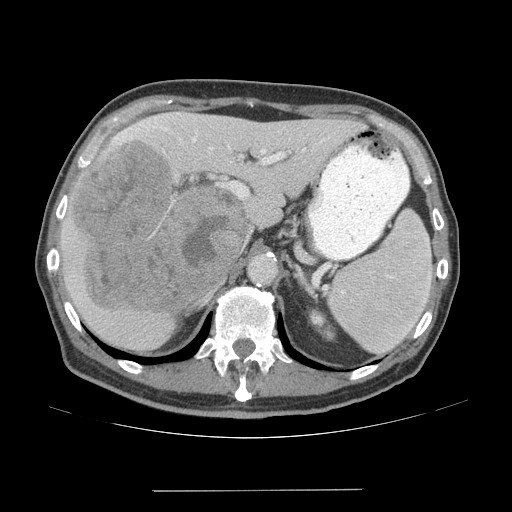
Contrast-enhanced abdominal CT (liver protocol), one axial slice; reconstruction kernel STANDARD; 140 kVp; soft-tissue window (W 400 / L 40 HU); 2.5 mm slice thickness; 512 × 512 image matrix. Case-level facts recorded for this patient, not image findings: diagnosis: hepatocellular carcinoma (patient treated with transarterial chemoembolisation; whether this scan precedes or follows treatment is not stated here); TNM stage (as recorded): Stage-IVA; Child-Pugh class: A; tumour nodularity: uninodular.
Outlined on this slice (semi-automatic segmentation, software-assisted and operator-edited):
- liver parenchyma outside the tumour (the mass and vessels are separate outlines, so this box may not span the whole liver): bounding box <60,110,361,350> (left, top, right, bottom; pixels)
- mass: <68,139,249,313>
- liver vessels: <112,113,325,164>